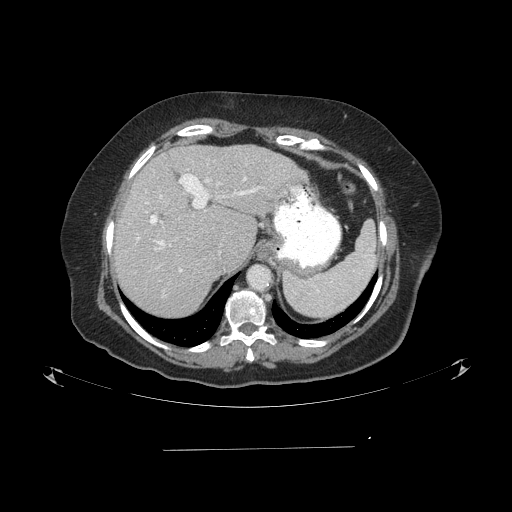
Contrast-enhanced abdominal CT (liver protocol), one axial slice. Slice 66 of 103 in the series (ordered by position). Reconstruction kernel STANDARD. 120 kVp. One of 2 acquisitions stored at this slice position. Soft-tissue window (W 400 / L 40 HU). 2.5 mm slice thickness. 512 × 512 image matrix, field of view 500 × 500 mm. Case-level facts recorded for this patient, not image findings: diagnosis: hepatocellular carcinoma (patient treated with transarterial chemoembolisation; whether this scan precedes or follows treatment is not stated here); TNM stage (as recorded): Stage-IIIA.
Annotated regions visible in this slice (semi-automatically segmented with operator editing):
- abdominal aorta: bounding box <248,265,271,289> (left, top, right, bottom; pixels)
- liver parenchyma outside the tumour (the mass and vessels are separate outlines, so this box may not span the whole liver): <114,144,306,316>
- liver vessels: <136,174,261,272>